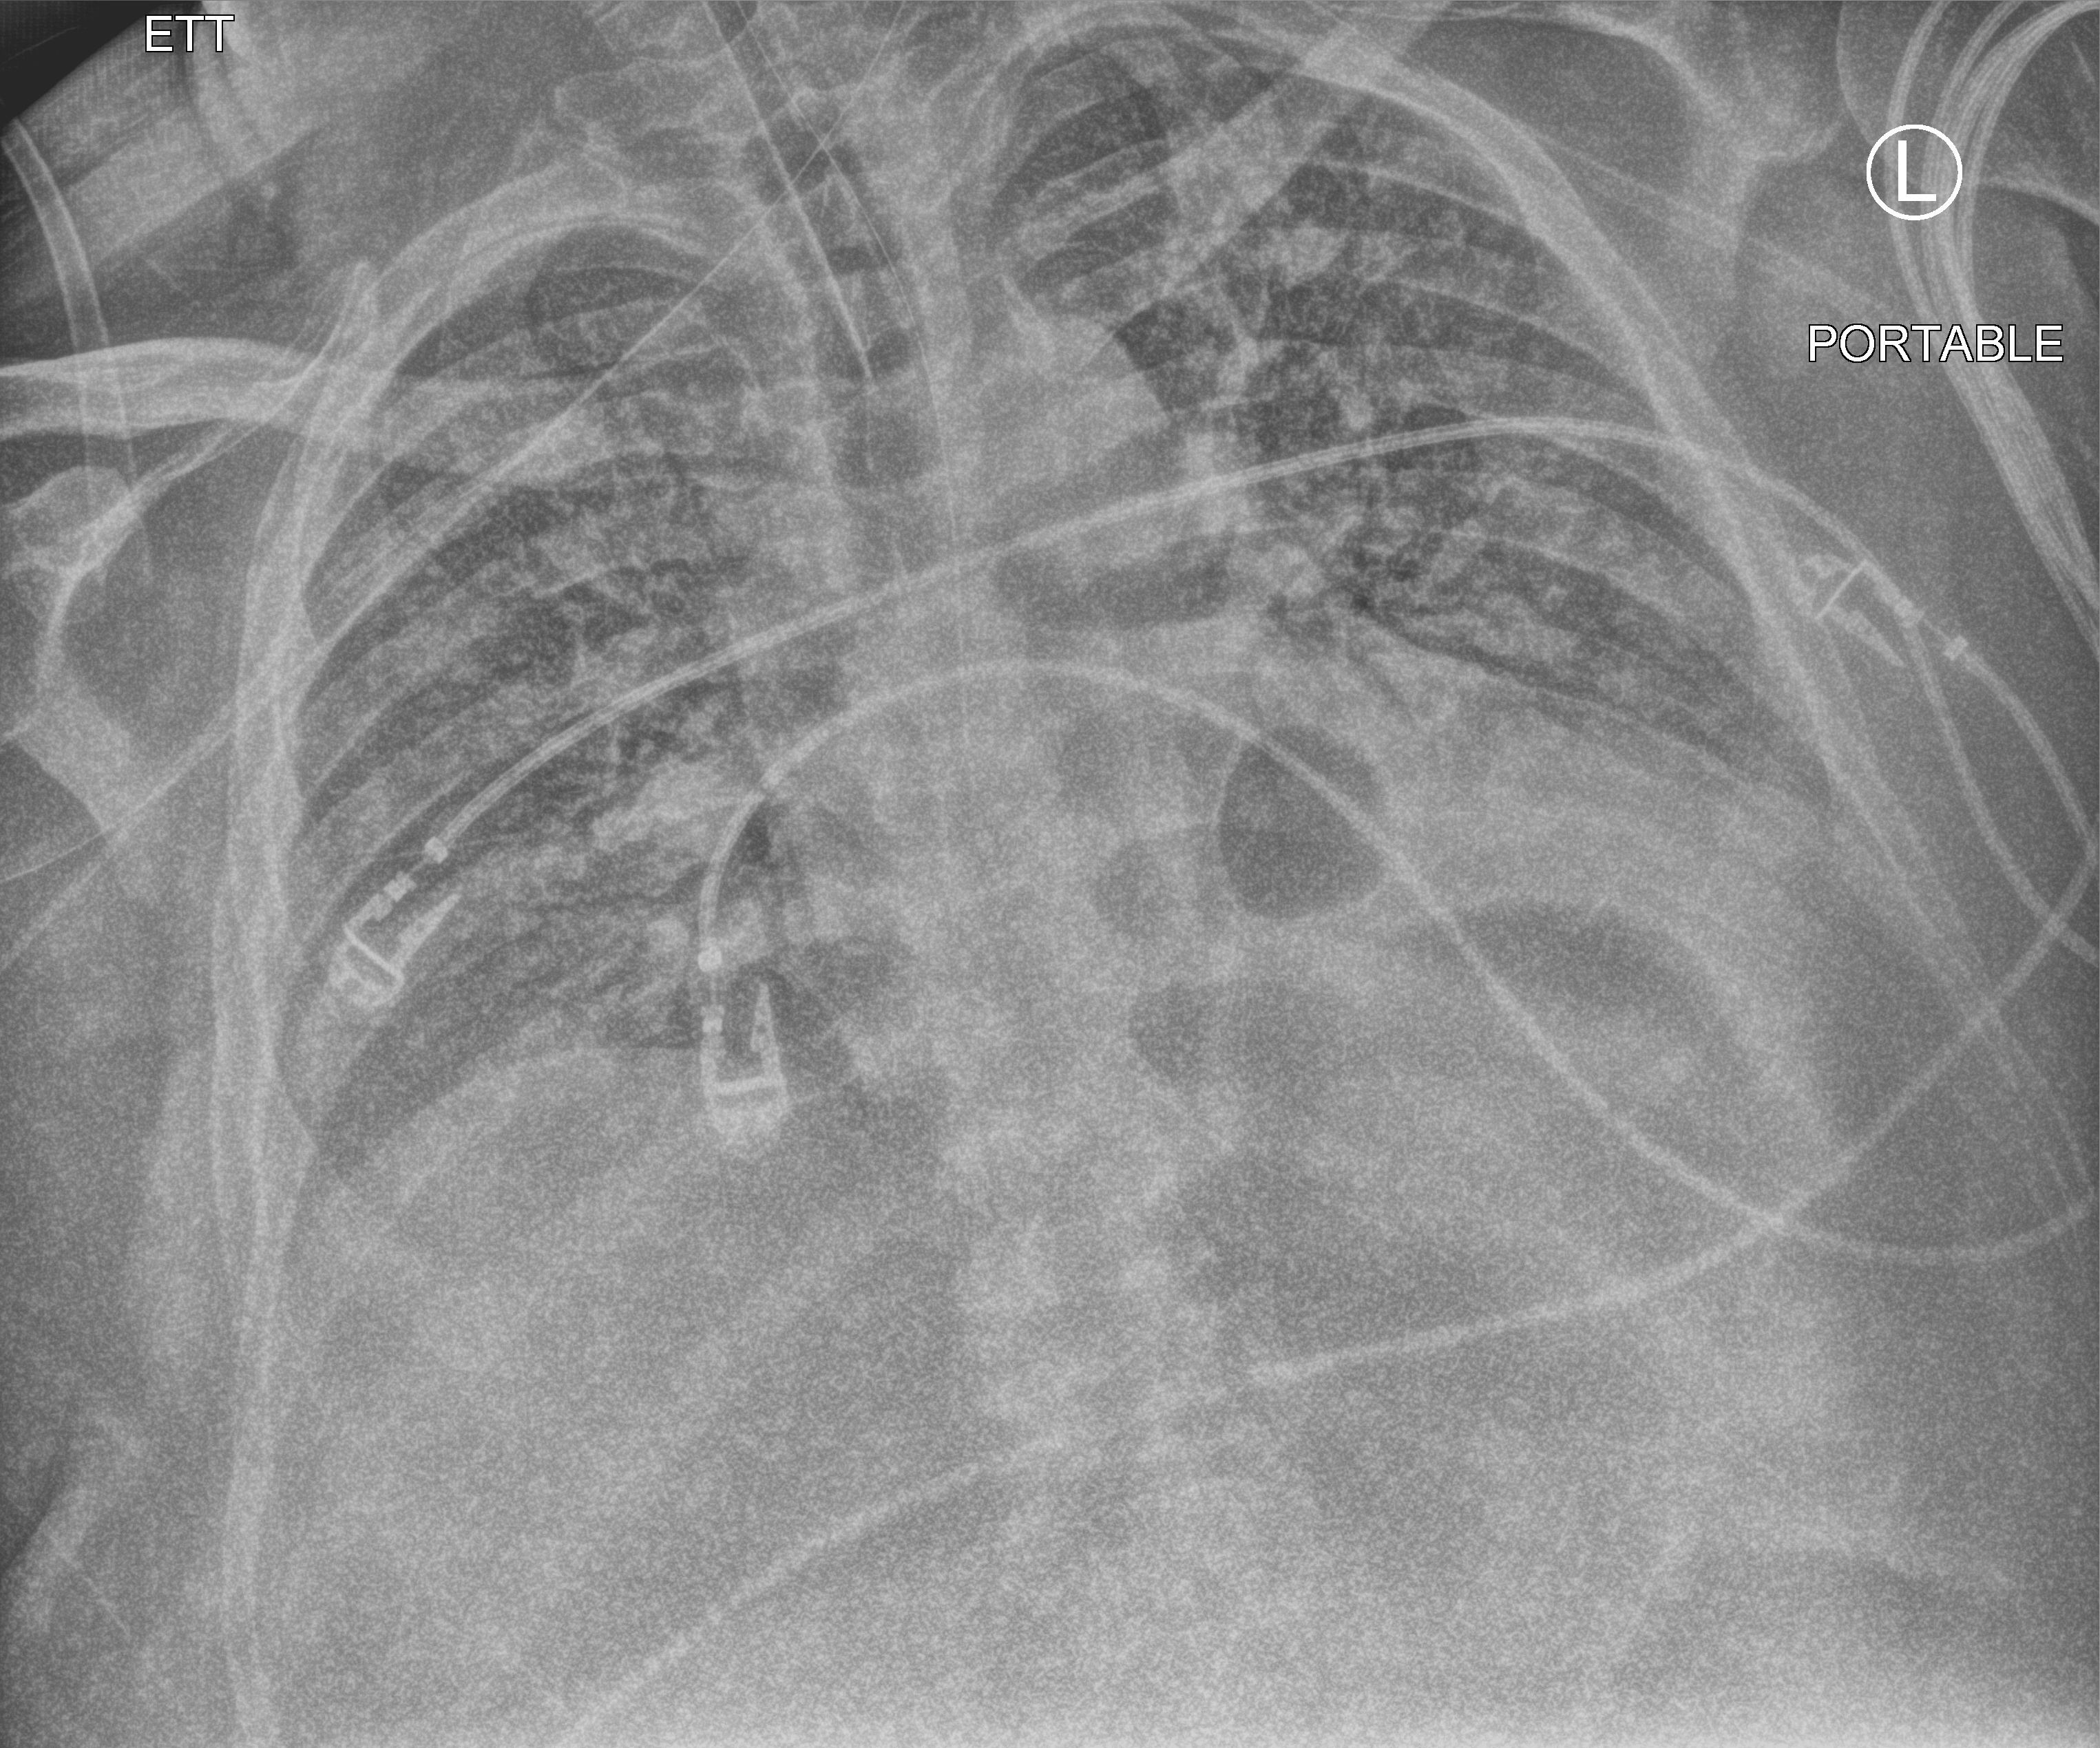
Portable chest radiograph; anteroposterior (AP) projection. Adult patient hospitalised with COVID-19, age 18–59 years.
Hospital-stay facts (about this admission, not read from this image; timing relative to this image not recorded):
- COPD (admission record): no